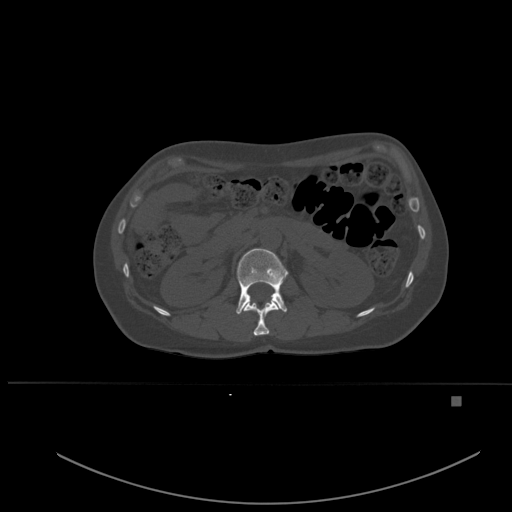
CT including the spine, one axial slice. Position 241 of 651 along the scan axis. Bone window (W 1800 / L 400 HU). 1.5 mm slice thickness. 512 × 512 image matrix, field of view 443 × 443 mm. Patient: female, 49 years. From the clinical record (not read from this slice): primary cancer: breast.
Outlined on this slice (semi-automatically segmented with operator editing):
- L1 vertebra: bounding box [x1, y1, x2, y2] px = [236, 248, 288, 315]
- T12 vertebra: [243, 300, 278, 336]